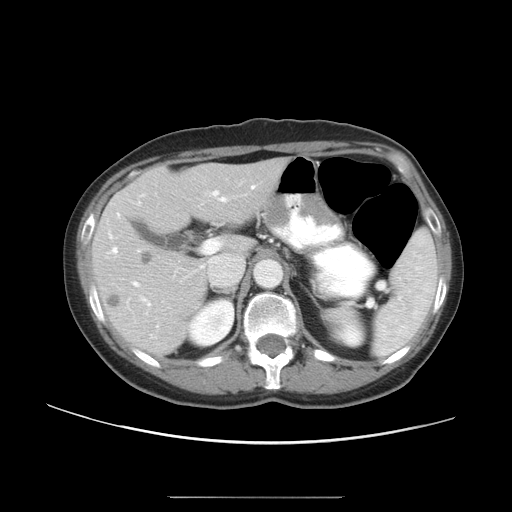
Contrast-enhanced abdominal CT, one axial slice; position 29 of 50 along the scan axis; reconstruction kernel STANDARD; intravenous contrast given; soft-tissue window (W 400 / L 40 HU); 512 × 512 image matrix. Female patient, age 58 years. From the clinical record (not read from this slice): diagnosis: colorectal cancer liver metastases, imaged before liver resection; multiple liver metastases: yes; largest metastasis: 7.3 cm; disease in both lobes: yes.
Outlined on this slice (manually delineated by an expert):
- hepatic veins: bounding box <113,186,255,253> (left, top, right, bottom; pixels)
- liver: <94,160,285,356>
- planned liver remnant (the part of the liver to remain after resection): <175,160,285,252>
- portal vein (with intrahepatic branches): <133,191,218,305>
- liver metastasis: <108,294,121,310>
- liver metastasis: <109,295,120,310>
- liver metastasis: <109,254,152,310>
- liver metastasis: <142,252,152,263>